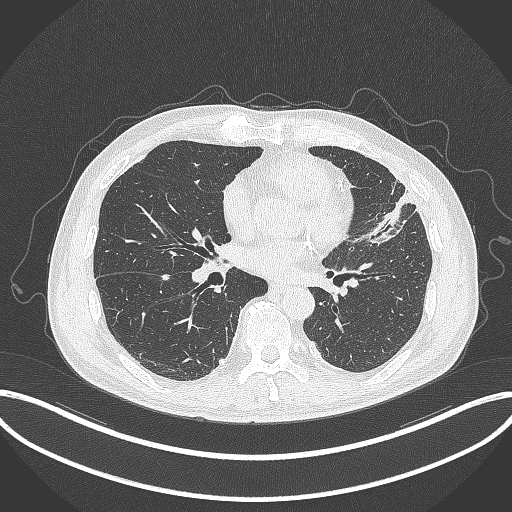
Chest CT, one axial slice; slice 150 of 382 in the series (ordered by position); 120 kVp; lung window (W 1500 / L -600 HU); 512 × 512 image matrix. Male patient, age 64 years. Case-level facts recorded for this patient, not image findings: clinical TNM (as recorded): T4 N1 M0.
Outlined on this slice (rectangle marked by the reading radiologist):
- lung tumour (recorded histology: adenocarcinoma): bounding box (x1, y1, x2, y2) in pixels: (366, 183, 417, 249)